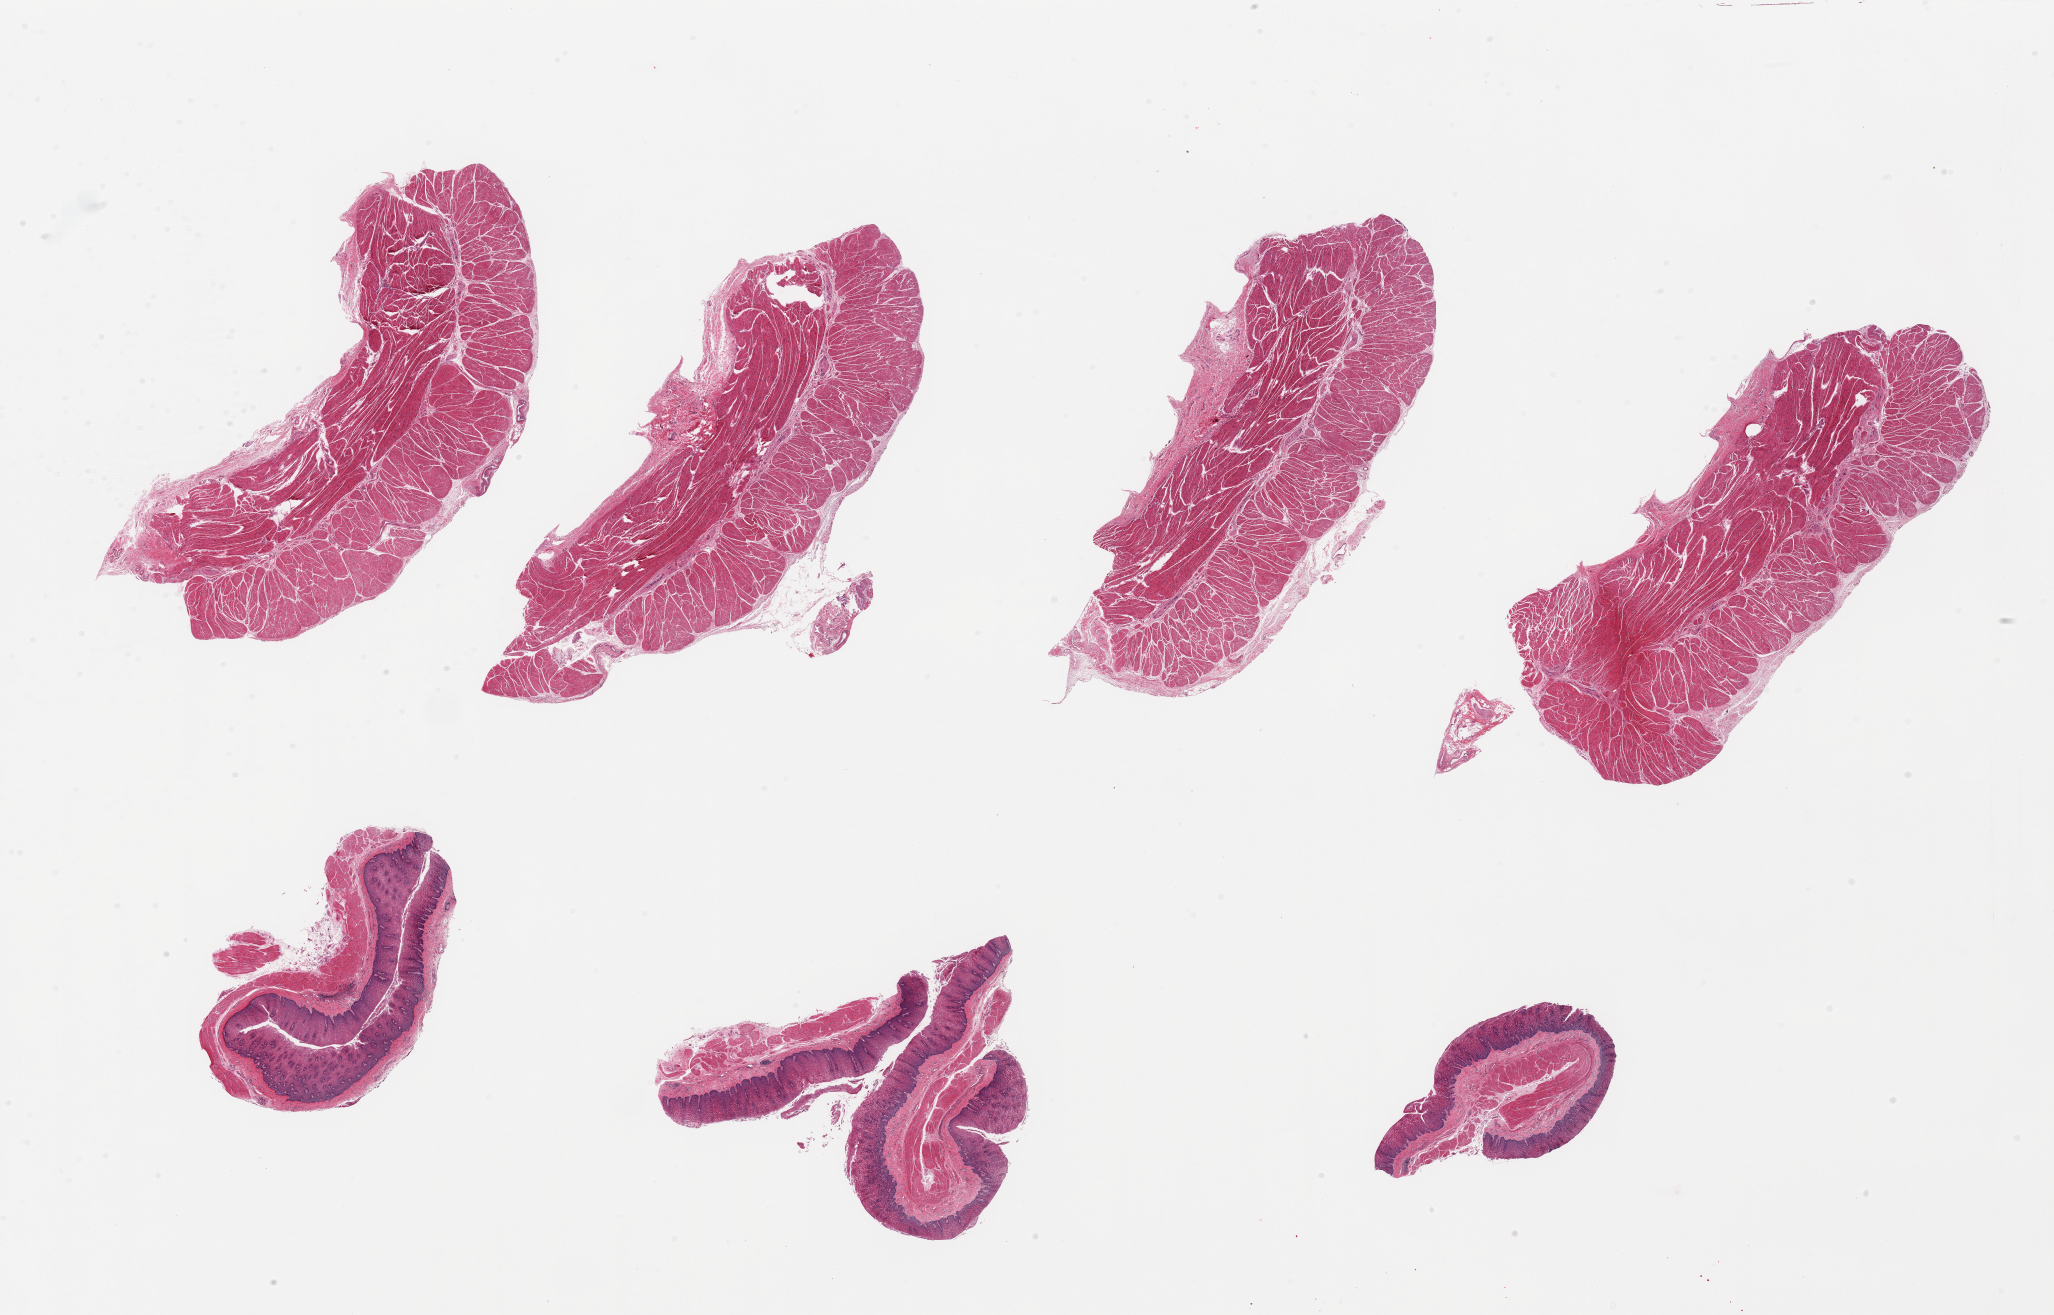
Digitized haematoxylin and eosin-stained section — whole scanned area (about 32.5 x 20.8 mm, slide scanned at 20x) shown as a low-resolution overview; PAXgene-fixed, paraffin-embedded tissue; target tissue: gastroesophageal junction; tissue donor sample. Donor sex: female.
Pathologist's review note for this sample: 7 pieces, 3 small fragments contaminantmucosa, avoid.